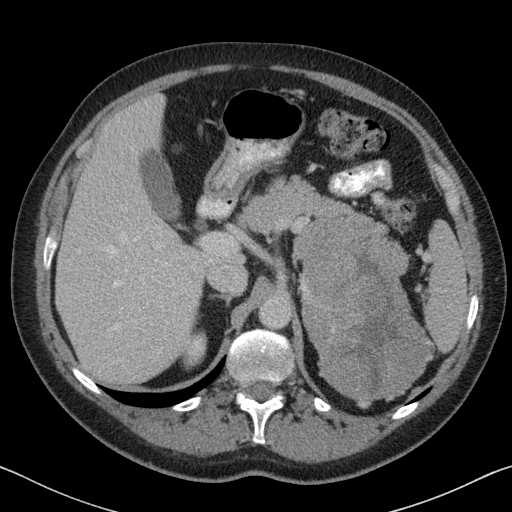
Contrast-enhanced abdominal CT, one axial slice. Slice 53 of 88 in the series (ordered by position). Reconstruction kernel B31f. Soft-tissue window (W 400 / L 40 HU). 512 × 512 image matrix, field of view 366 × 366 mm. Patient: male, 51 years. From the clinical record (not read from this slice): diagnosis: adrenocortical carcinoma; tumour side: left adrenal; tumour size at pathology: 16.5 cm; Ki-67 index: 30 %; stage (as recorded): 2.
Annotated regions visible in this slice (semi-automatically segmented with operator editing):
- mass: bounding box (x1, y1, x2, y2) in pixels: (295, 220, 434, 405)